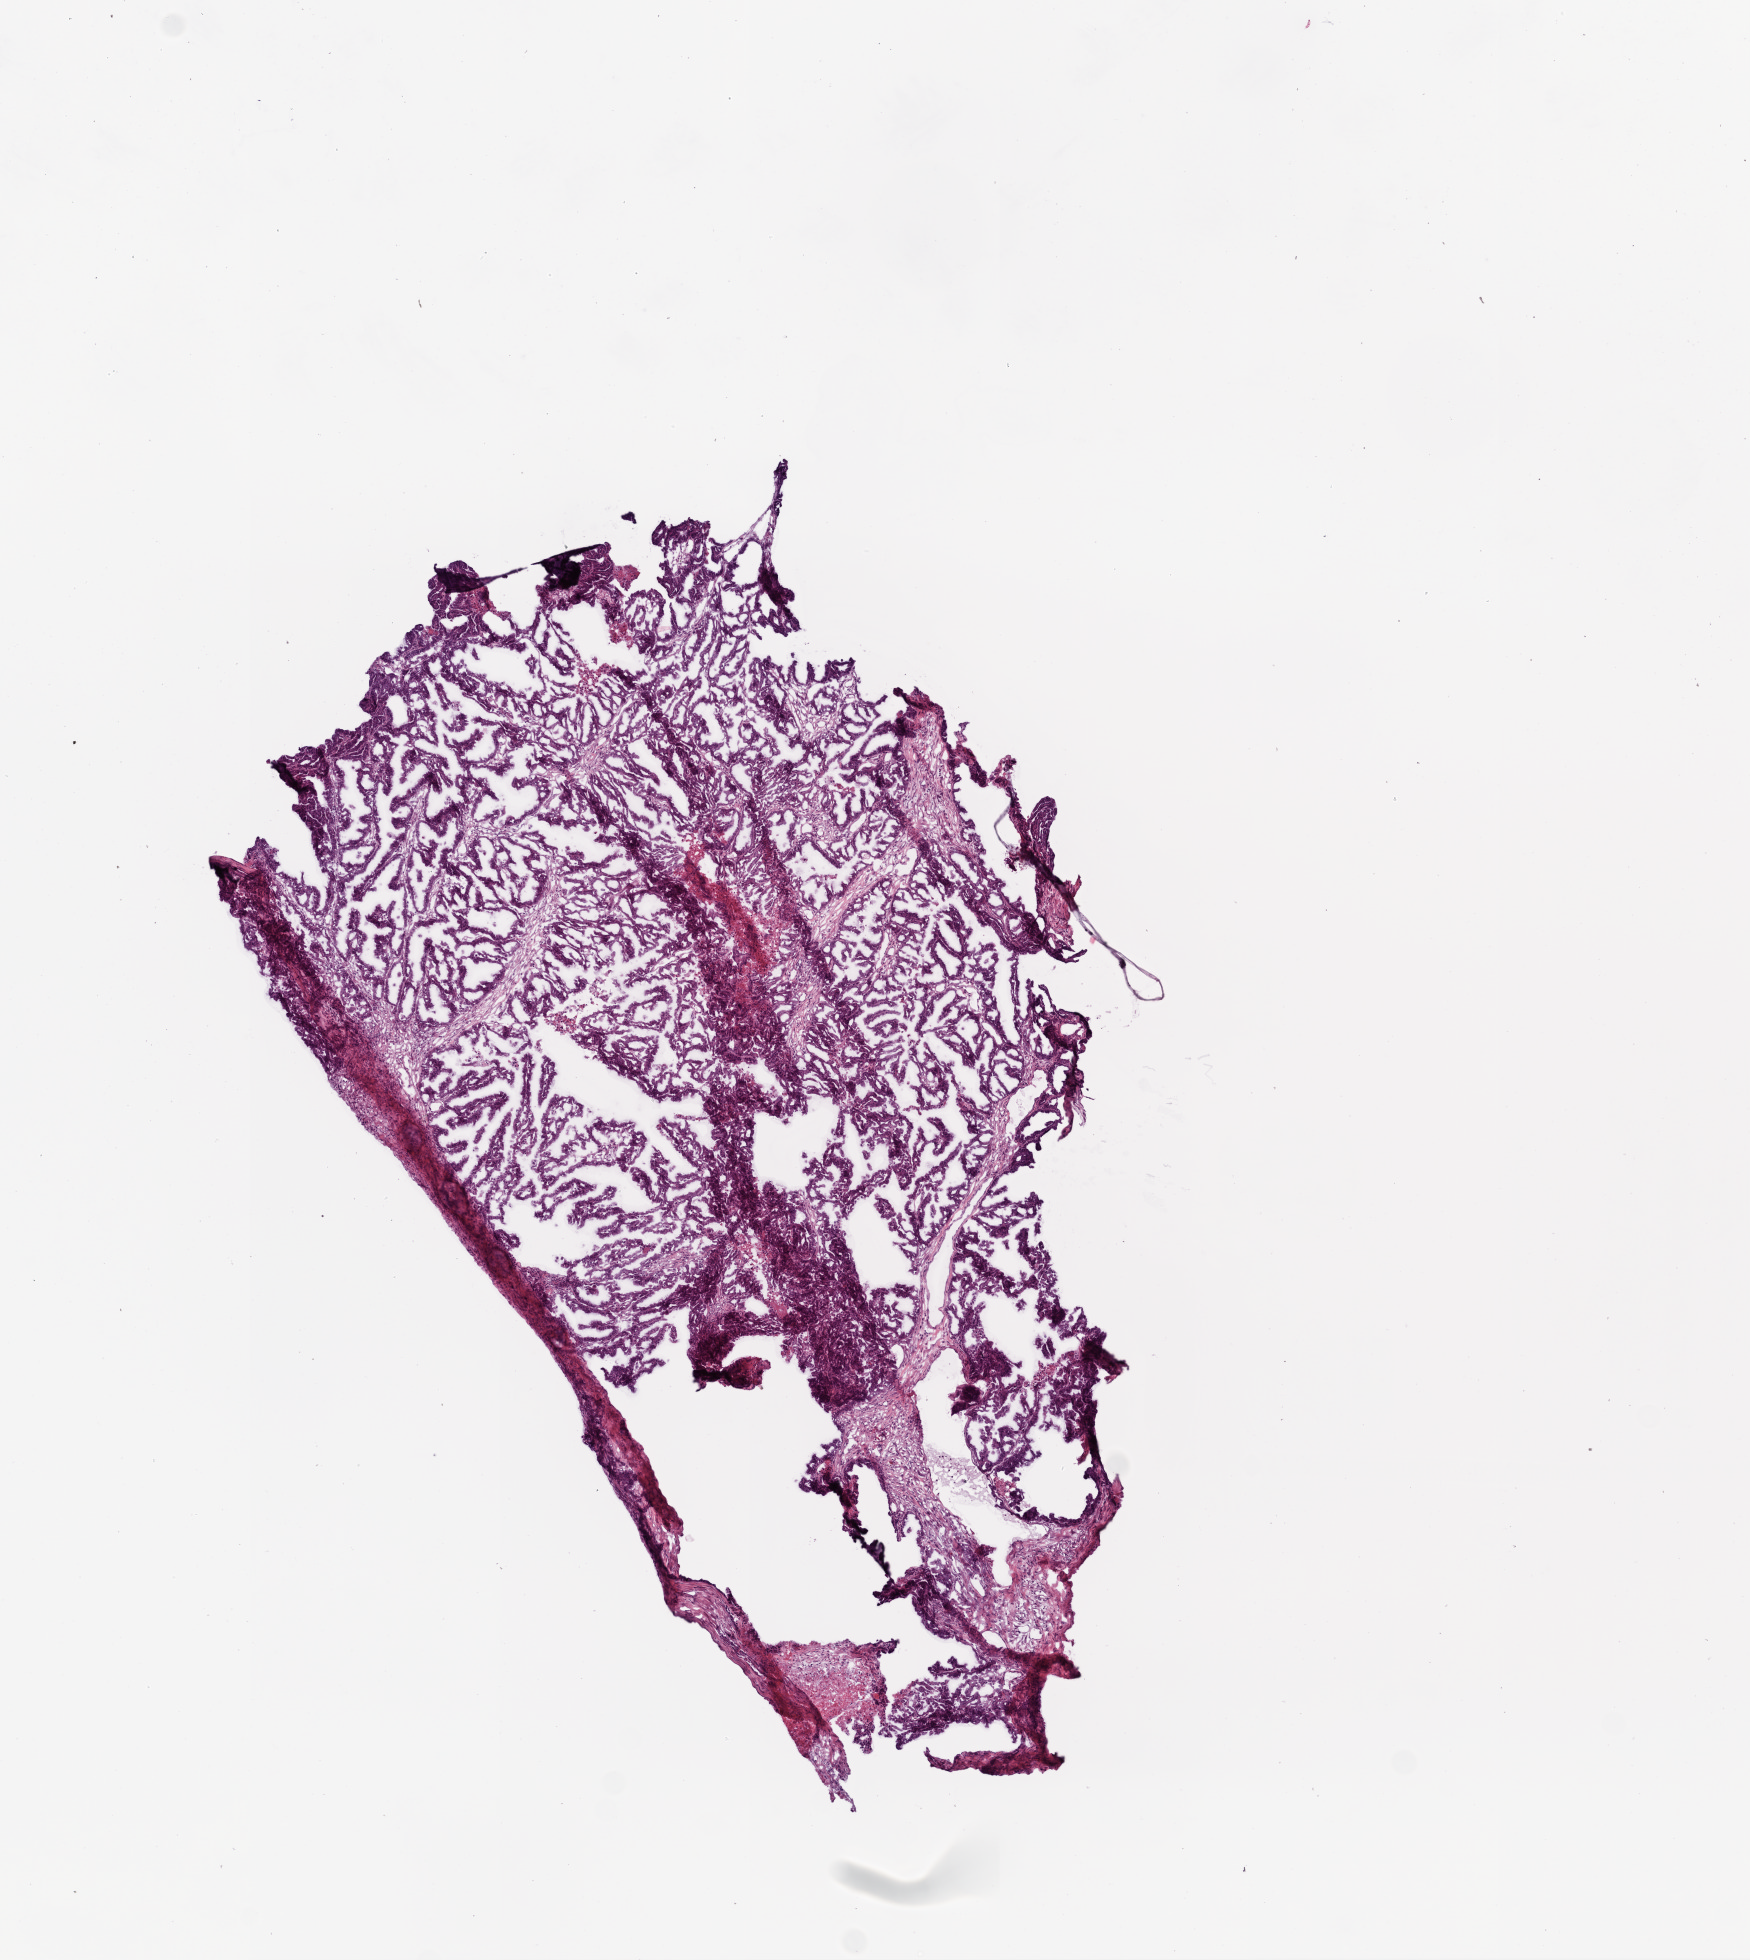
Digitized H&E tissue section (whole slide), low-resolution overview of the scanned area, about 7.0 x 7.9 mm, frozen section from the bottom of the tissue portion, primary tumour sample from the ovary. Female, age 44 years at initial diagnosis. Histologic grade: G3 (poorly differentiated). Pathologist review of this section (percent, as recorded): tumour cells 79%, tumour nuclei 80%, normal cells 1%, stromal cells 19%, necrosis 1%.
- pathologic diagnosis: Serous cystadenocarcinoma, NOS
- FIGO stage: IV
- laterality: bilateral